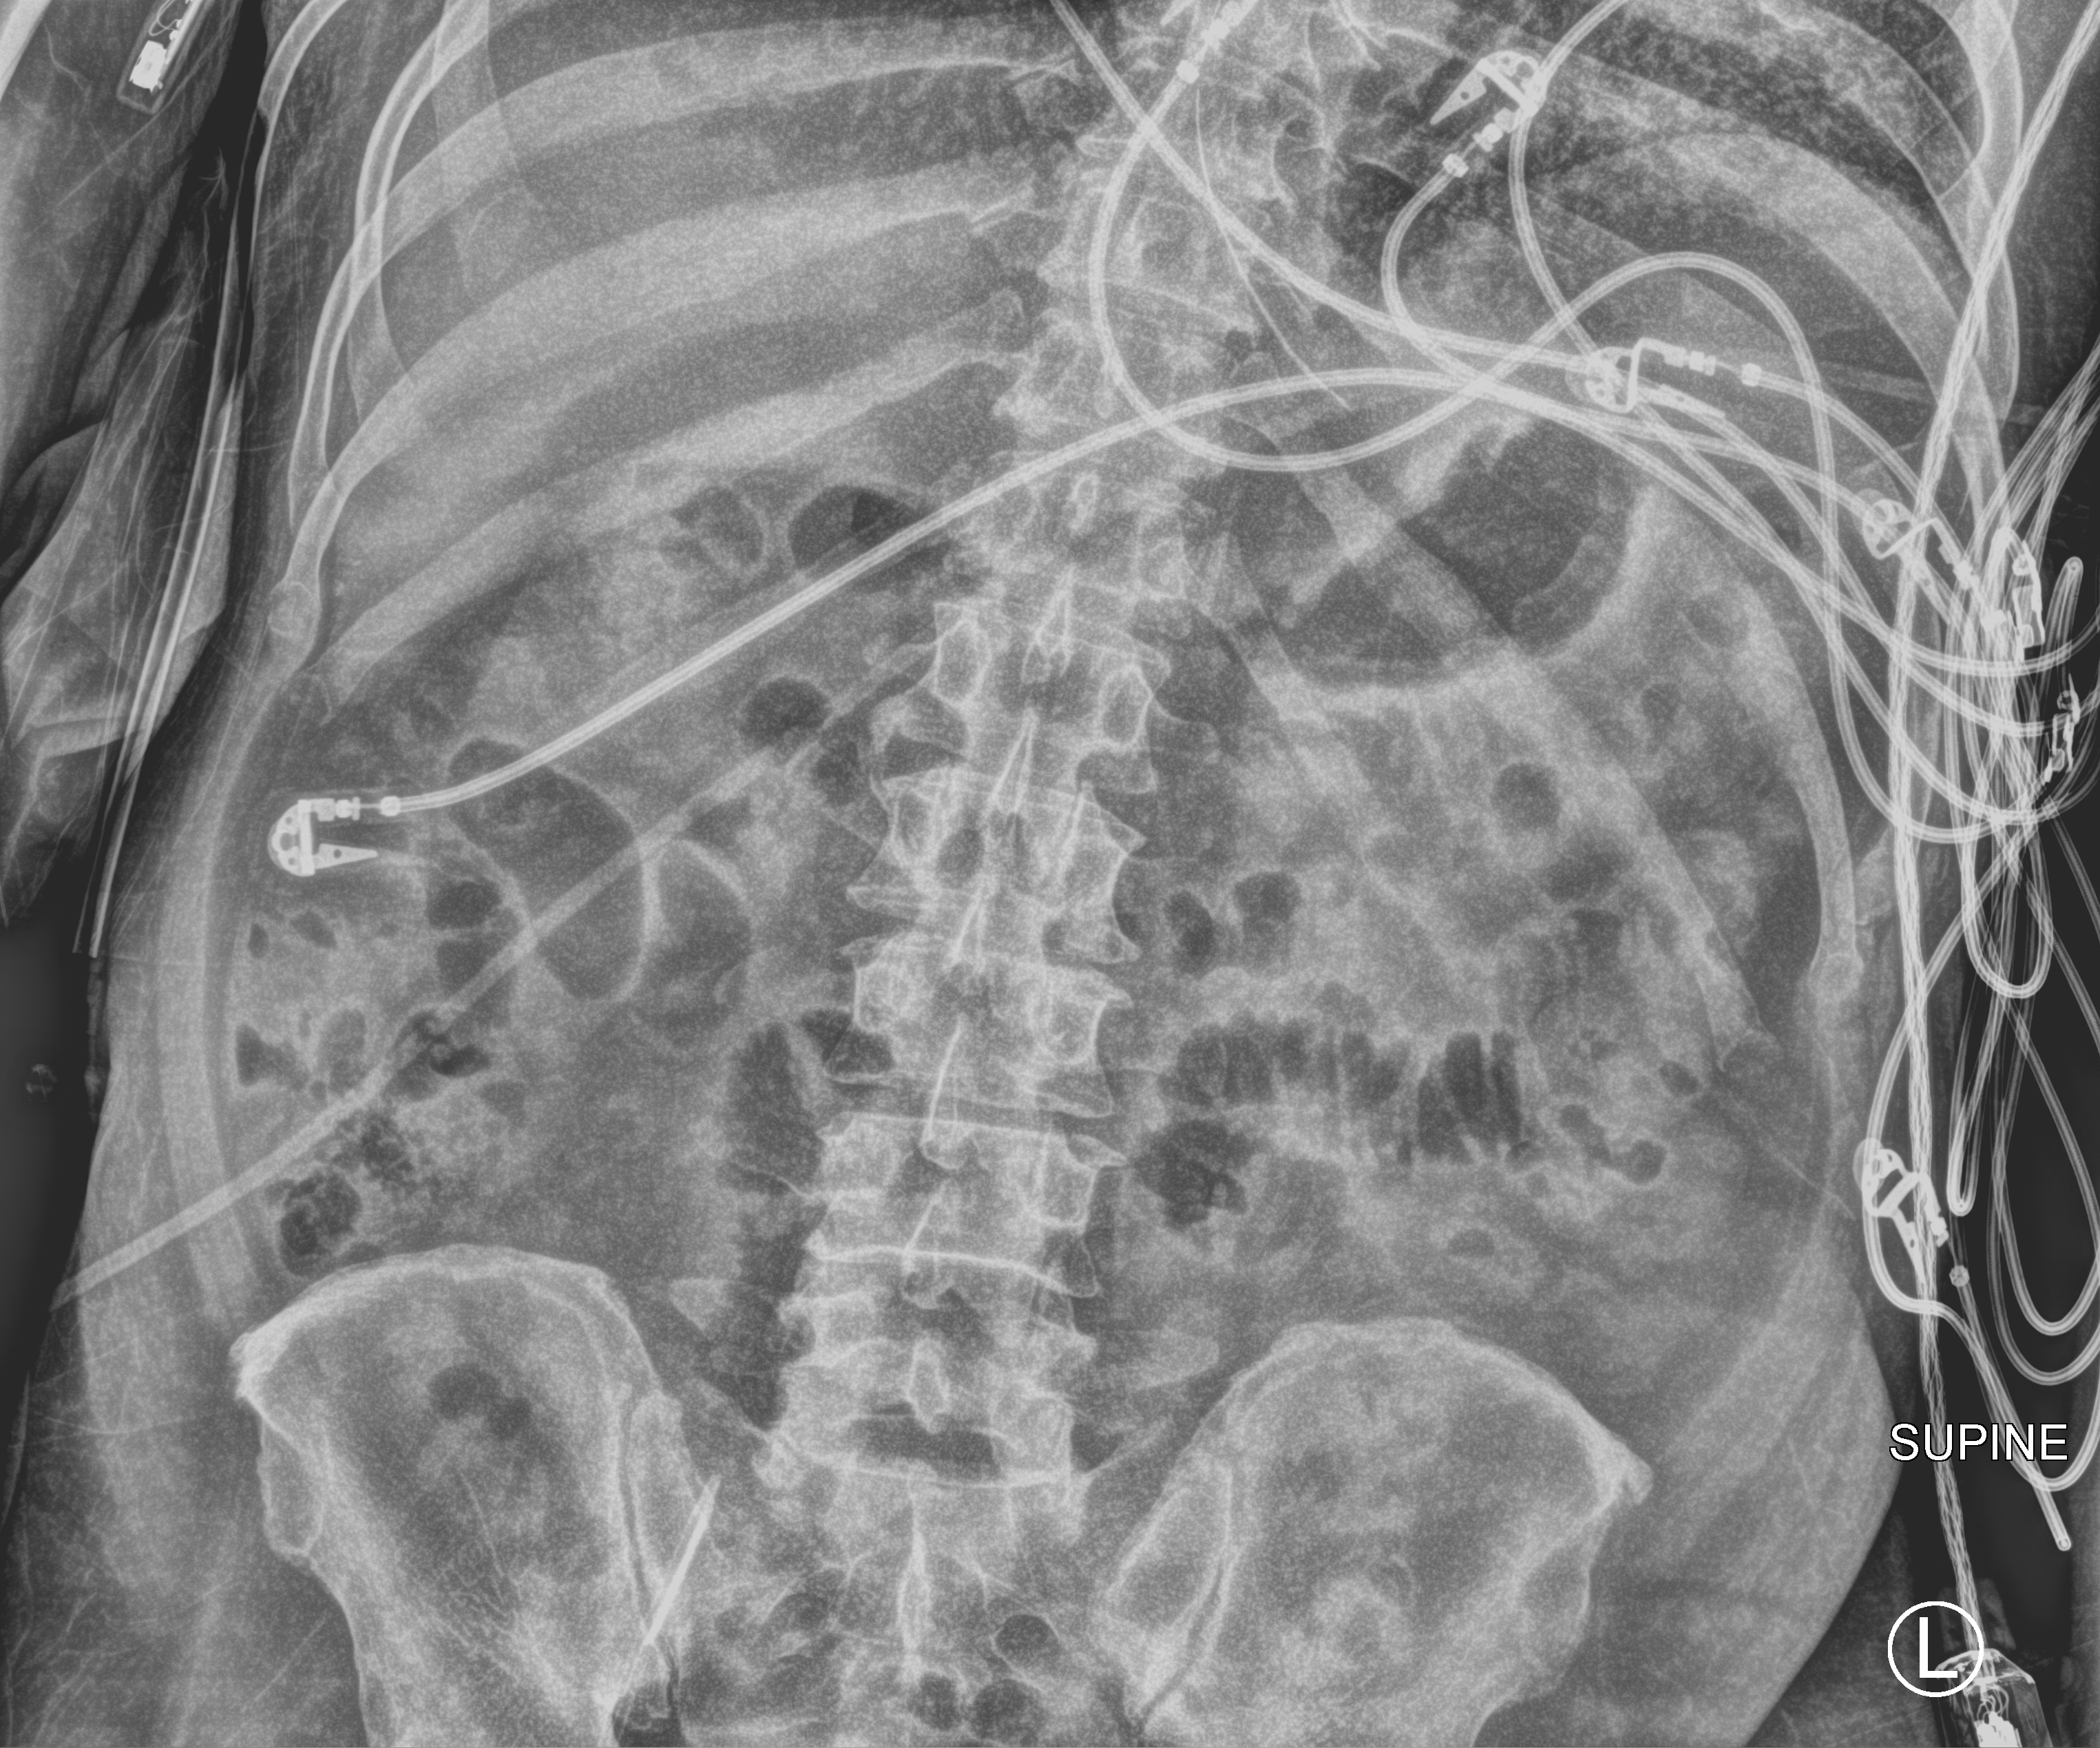
Portable abdomen radiograph. Male patient hospitalised with COVID-19, age 18–59 years.
Admission-level facts for this patient (not findings on this image; timing relative to this image not recorded):
- hypertension (admission record): no
- mechanically ventilated during this hospital stay: yes